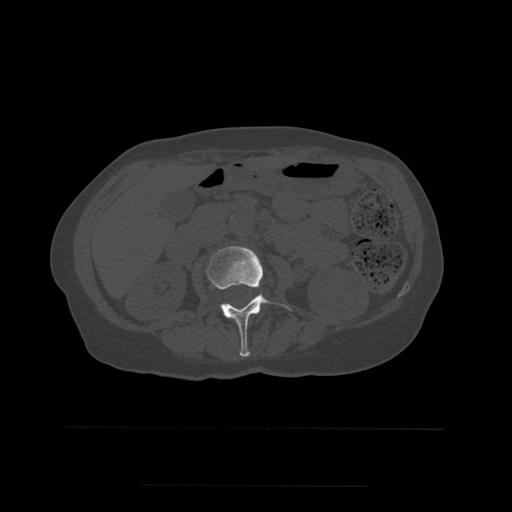
CT including the spine, one axial slice. Position 208 of 544 along the scan axis. Bone window (W 1800 / L 400 HU). 1.25 mm slice thickness. 512 × 512 image matrix. Patient age 58 years. Case-level facts recorded for this patient, not image findings: primary cancer: lung.
Structures marked on this image (semi-automatically segmented with operator editing):
- L2 vertebra: bounding box [x1, y1, x2, y2] px = [205, 246, 292, 357]